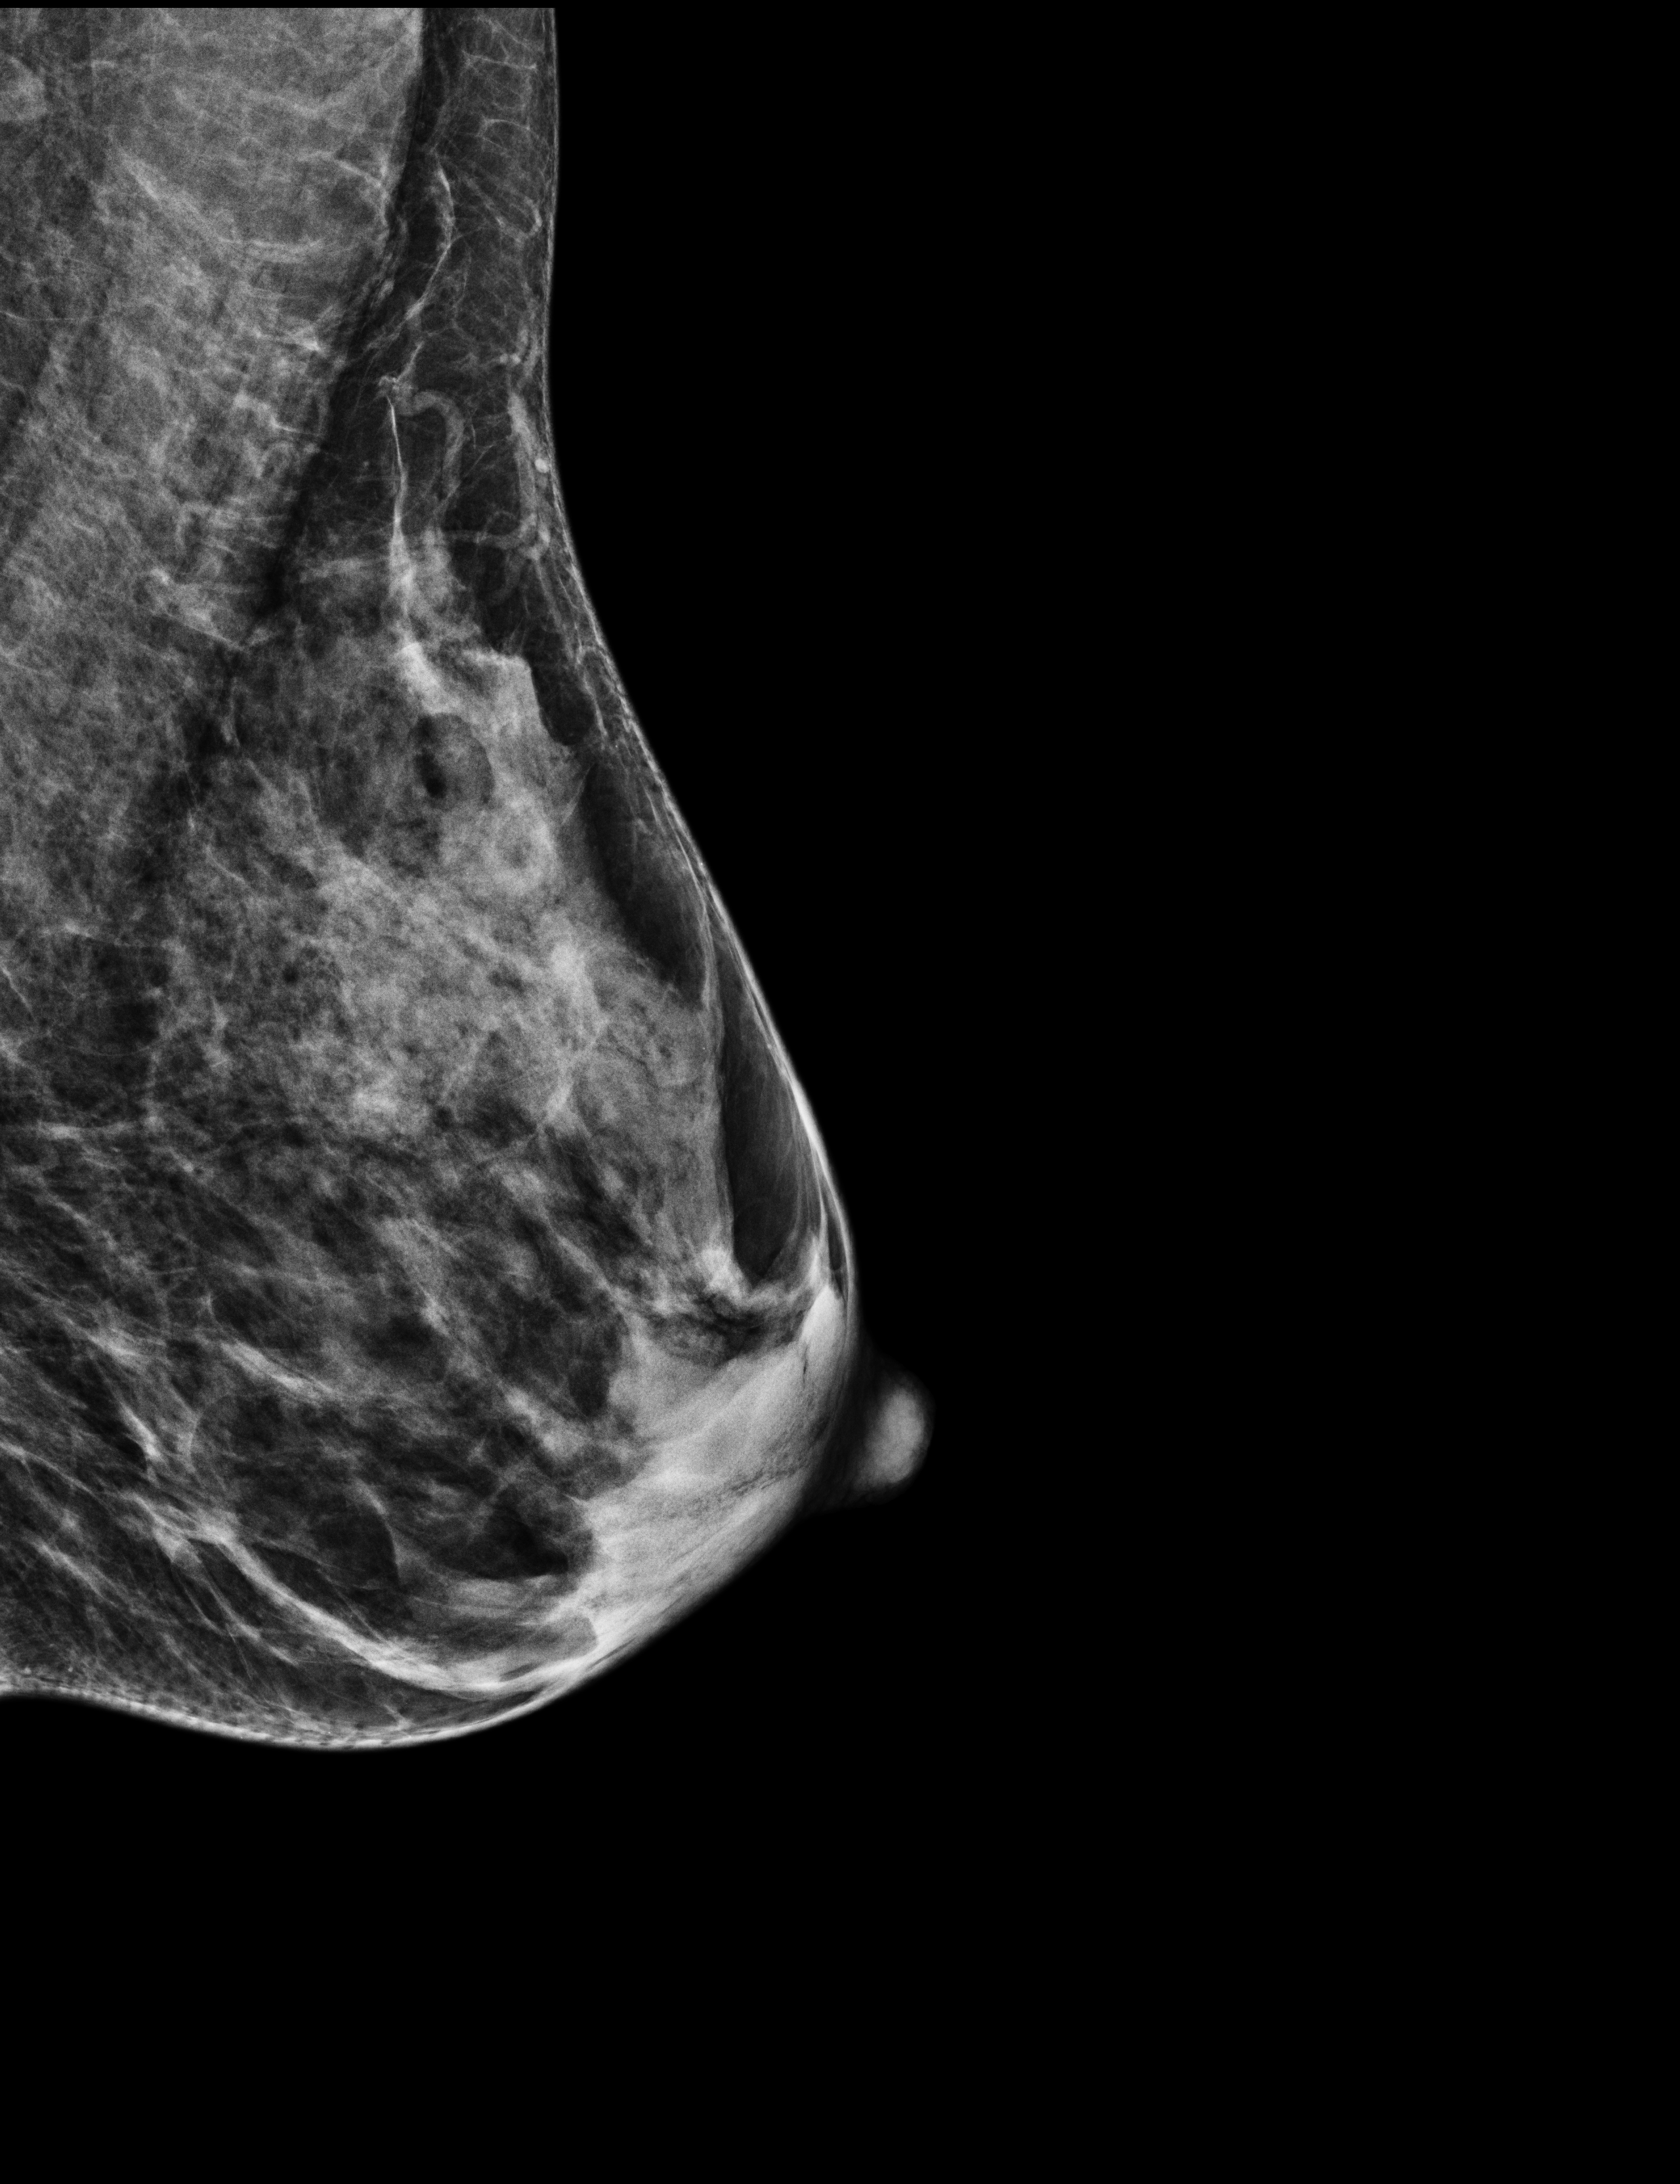
Annual screening mammography examination; compressed breast thickness 36 mm. Patient: female, 56 years.
Image type: full-field digital mammogram. Breast: left. Projection: MLO view.